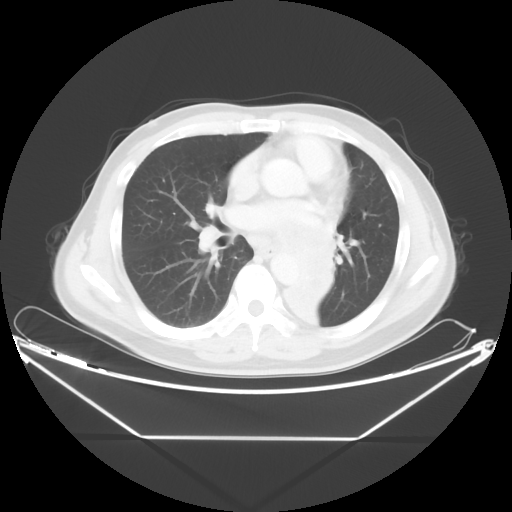
Chest CT, one axial slice; slice 23 of 48 in the series (ordered by position); lung window (W 1500 / L -600 HU); 5 mm slice thickness; 512 × 512 image matrix, field of view 438 × 438 mm. Patient: male, 58 years. From the clinical record (not read from this slice): clinical TNM (as recorded): T3 N3 M0.
Structures marked on this image (rectangle marked by the reading radiologist):
- lung tumour (recorded histology: squamous cell carcinoma): bounding box <284,204,356,348> (left, top, right, bottom; pixels)